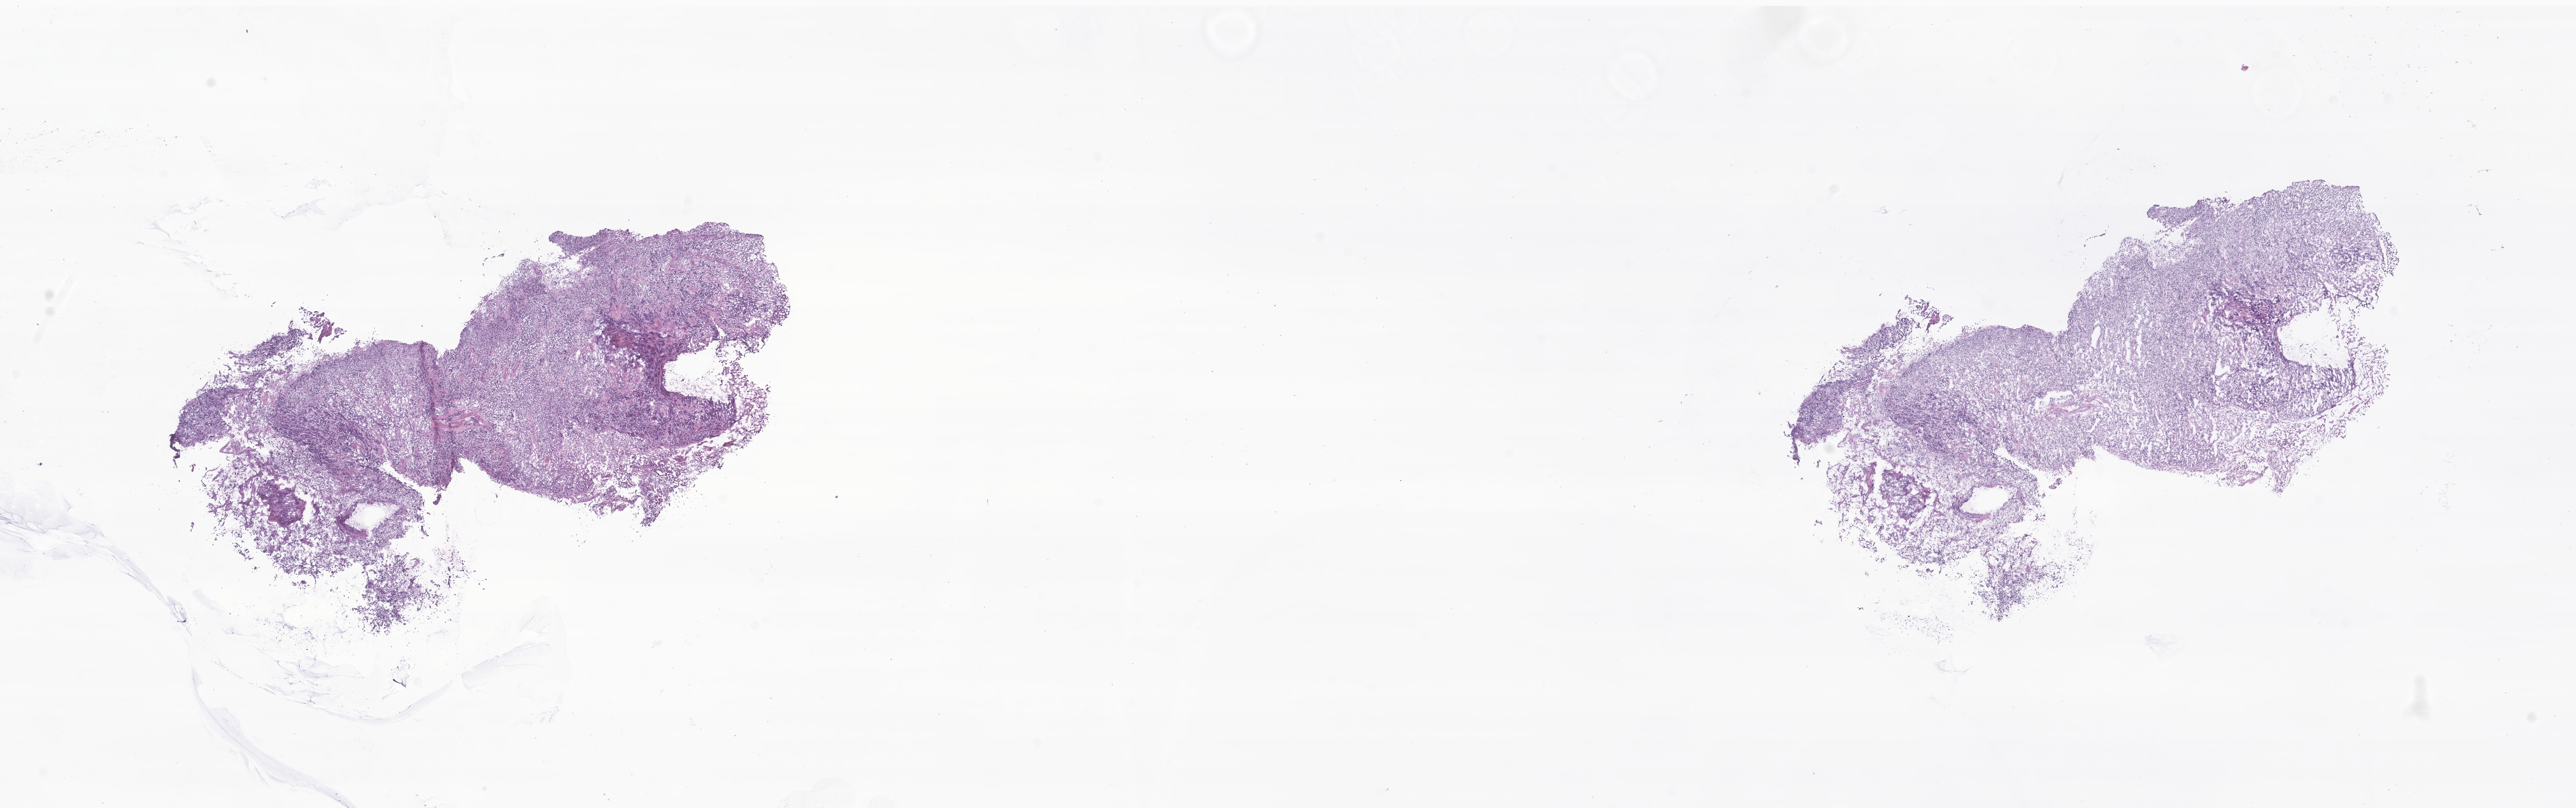
Whole-slide image, H&E stain of tumor tissue from the brain, low-resolution overview of the scanned area, about 27.1 x 8.5 mm, frozen section (OCT-embedded). Male patient, age 61 months.
- diagnosis: Medulloblastoma, NOS